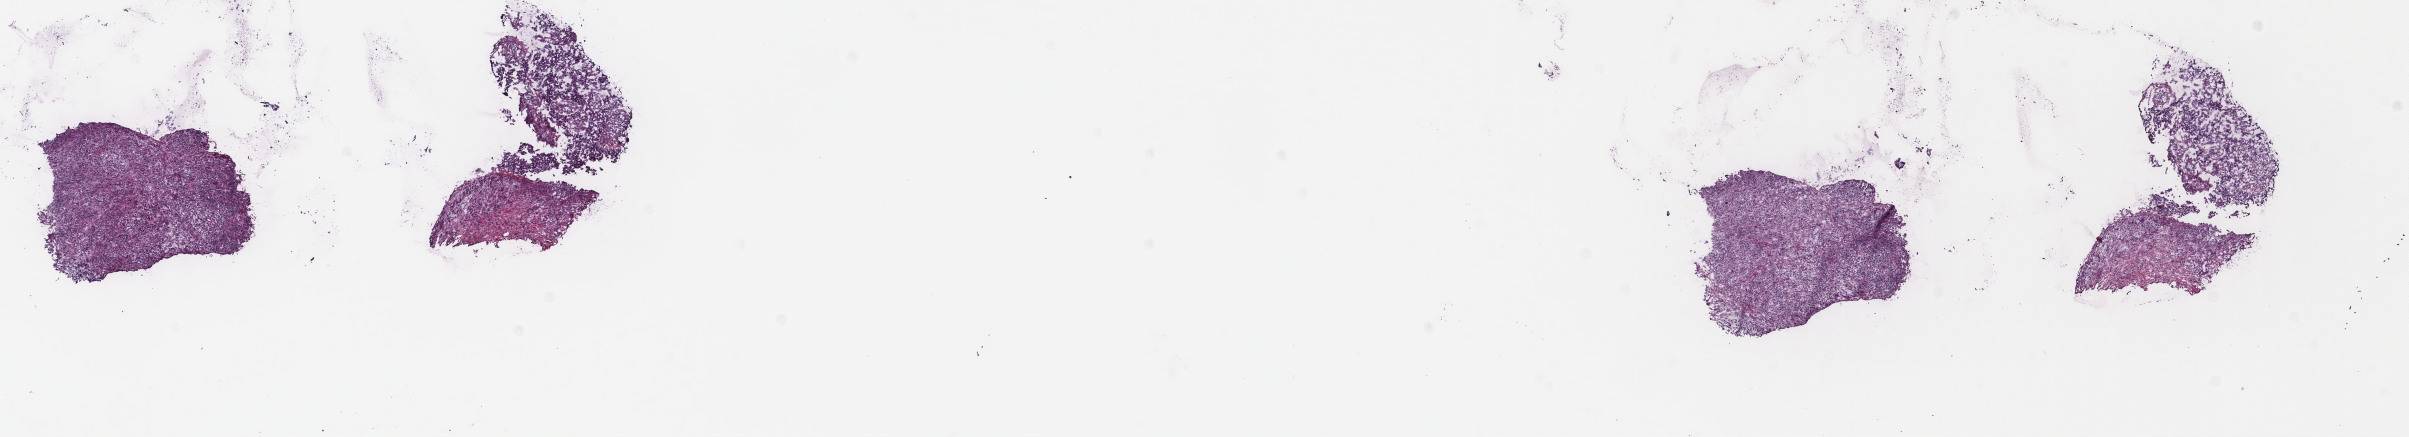
Whole-slide histology image, H&E — a low-resolution overview of the entire scanned area, about 19.1 x 3.5 mm (slide scanned at 40x); frozen section; sample: primary tumour, bladder. Female, age 78 years at initial diagnosis. Histologic grade: high grade. Composition of this section per pathologist review: tumour cells 50%, tumour nuclei 70%, normal cells 0%, stromal cells 47%, necrosis 3%. Inflammatory infiltration, as recorded: lymphocyte infiltration 6%, monocyte infiltration 1%, neutrophil infiltration 1%.
TNM: T3 N0 M0. AJCC pathologic stage: III. Histologic diagnosis: Transitional cell carcinoma (dome of bladder).